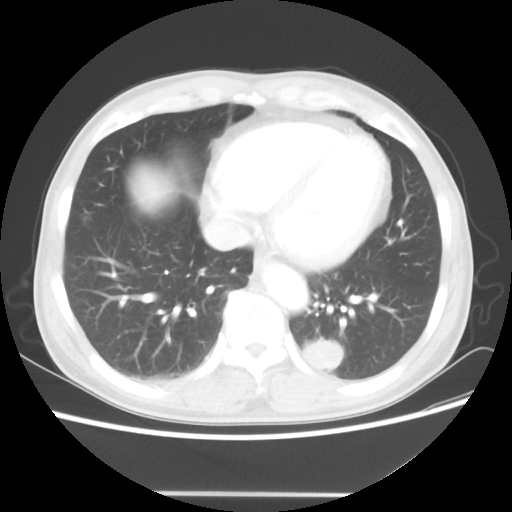
Chest CT, one axial slice. Position 18 of 60 along the scan axis. Reconstruction kernel STANDARD. 100 kVp. Lung window (W 1500 / L -600 HU). 5 mm slice thickness. 512 × 512 image matrix. Patient: male, 55 years. Case-level facts recorded for this patient, not image findings: clinical TNM (as recorded): T1c N3 M0.
Outlined on this slice (bounding box drawn by a radiologist):
- lung tumour (recorded histology: small cell carcinoma): bounding box [x1, y1, x2, y2] px = [301, 331, 345, 377]